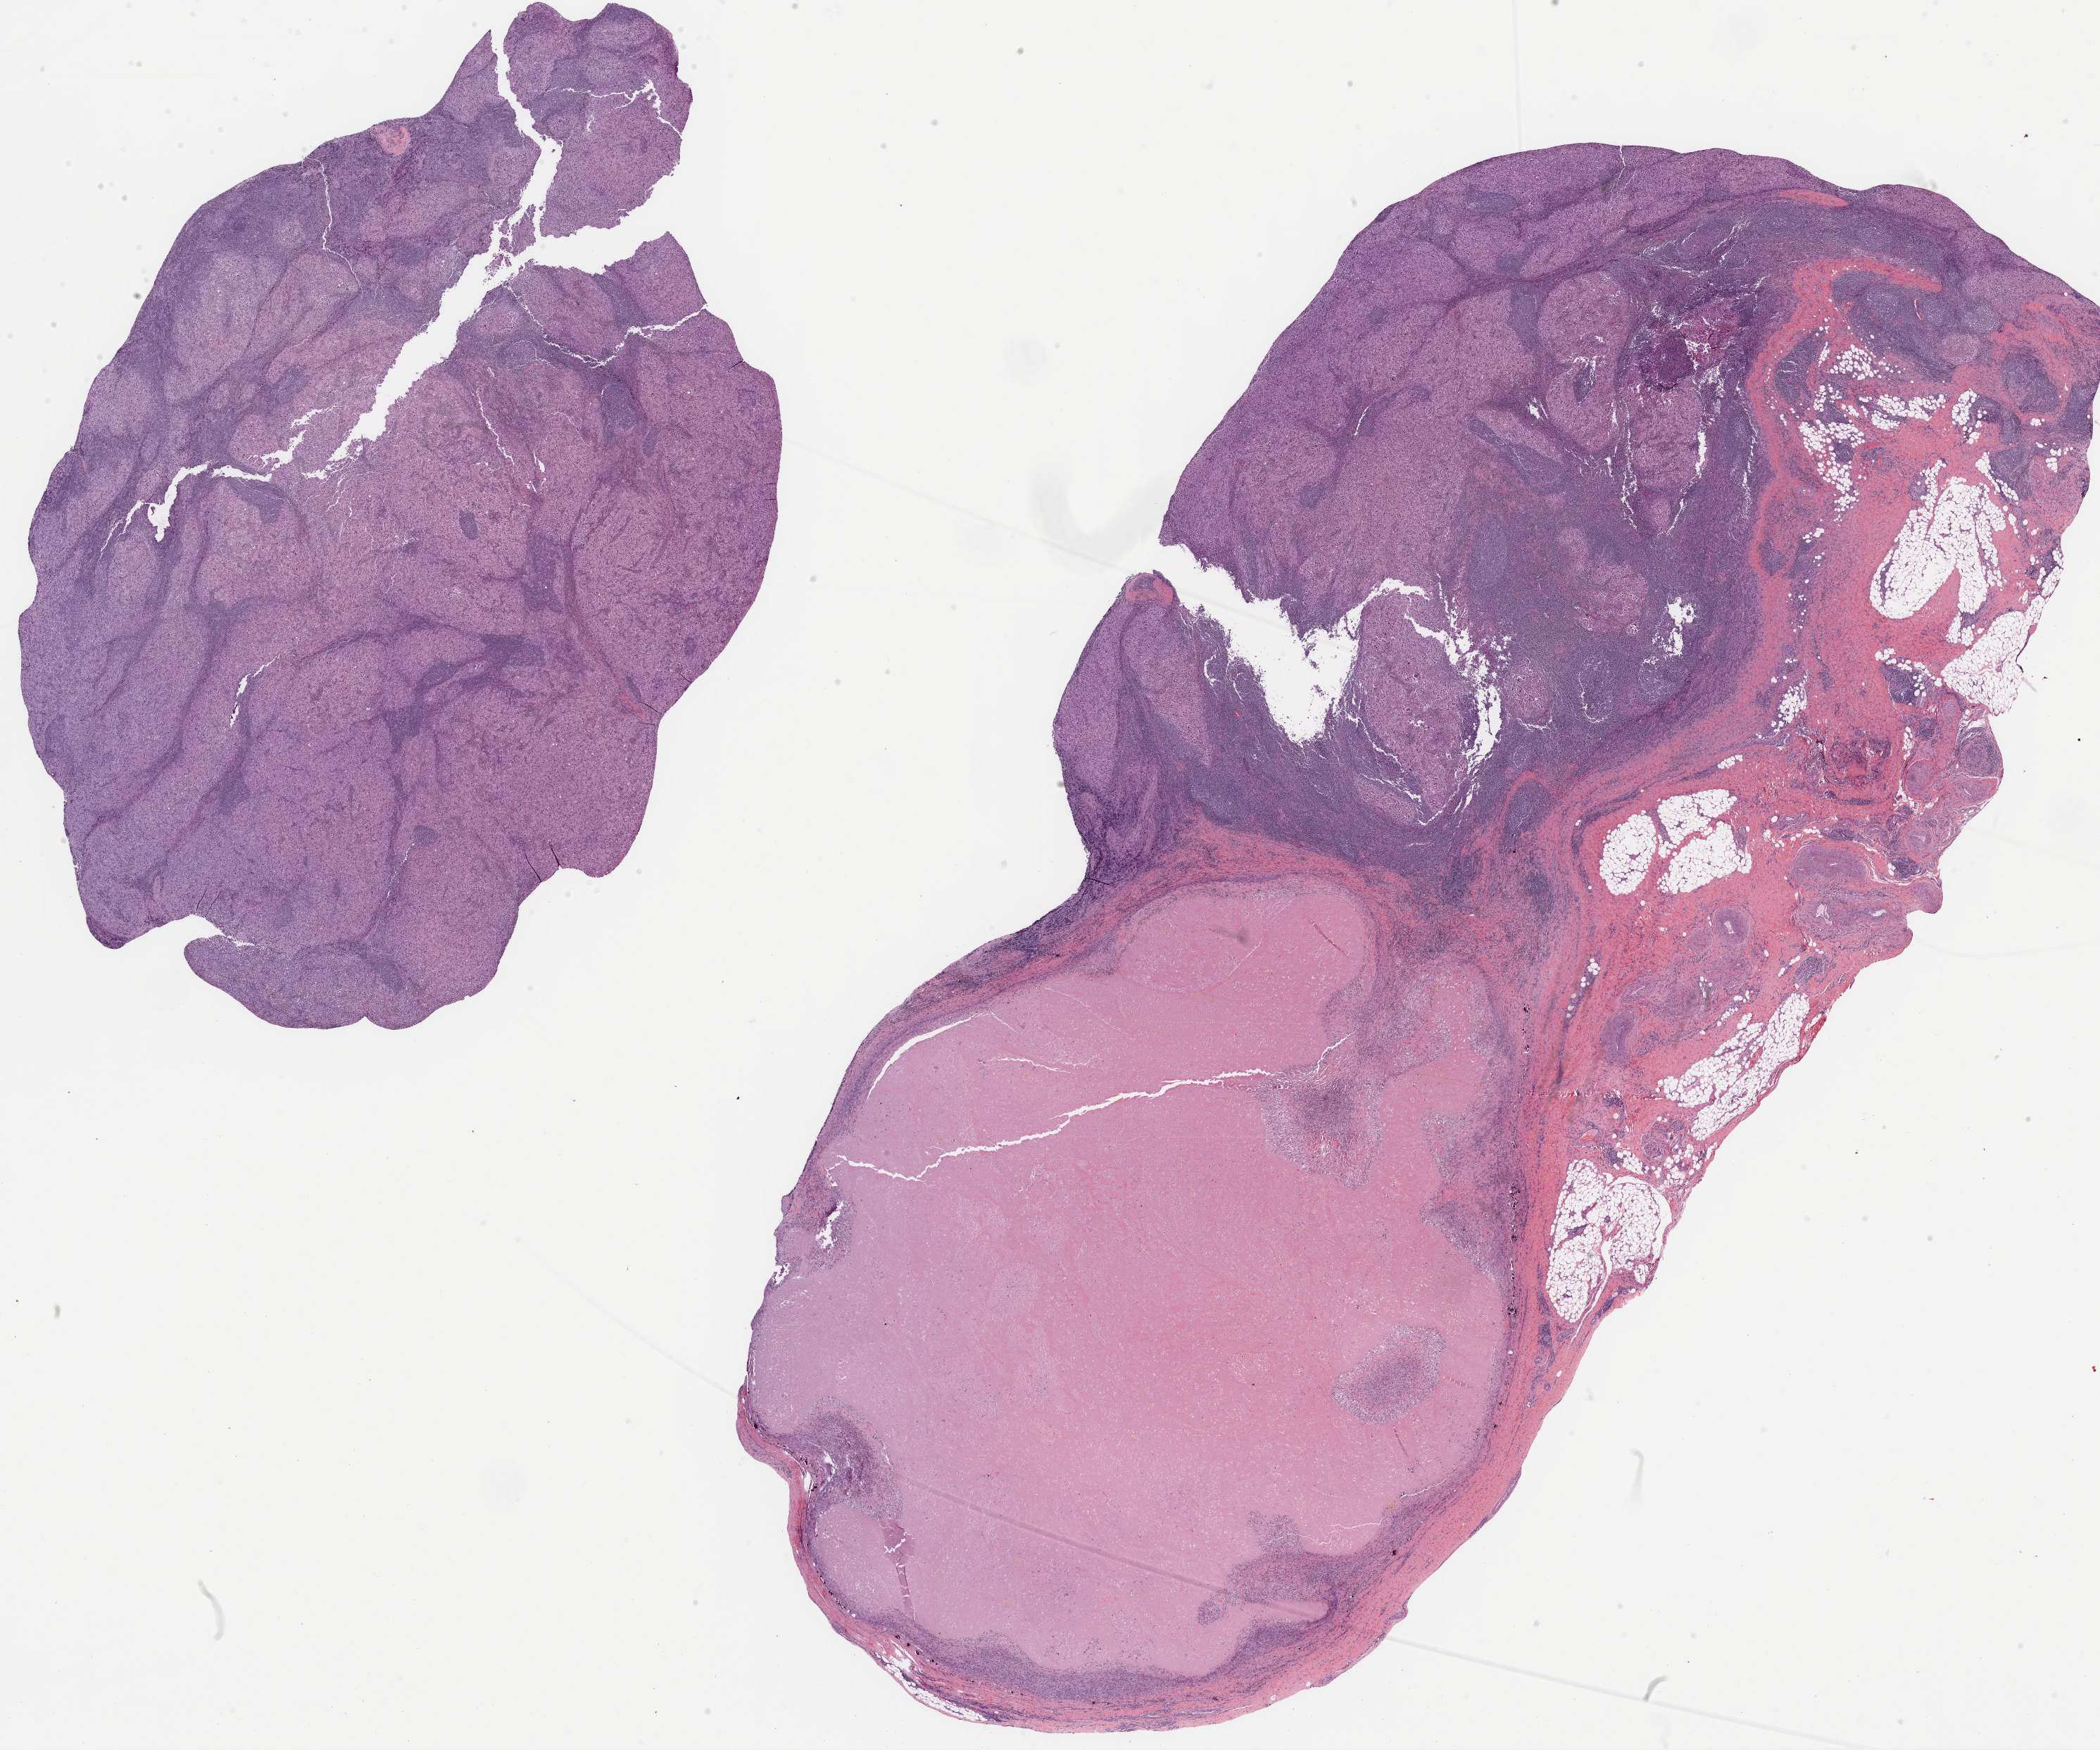
Hematoxylin and eosin (H&E) stained whole-slide image, a low-resolution overview of the entire scanned area, about 24.1 x 20.0 mm (slide scanned at 20x). FFPE section. Metastatic tumour sample. Male, age 60 years at initial diagnosis.
This section: metastatic tumour tissue. Patient diagnosis: Malignant melanoma, NOS.